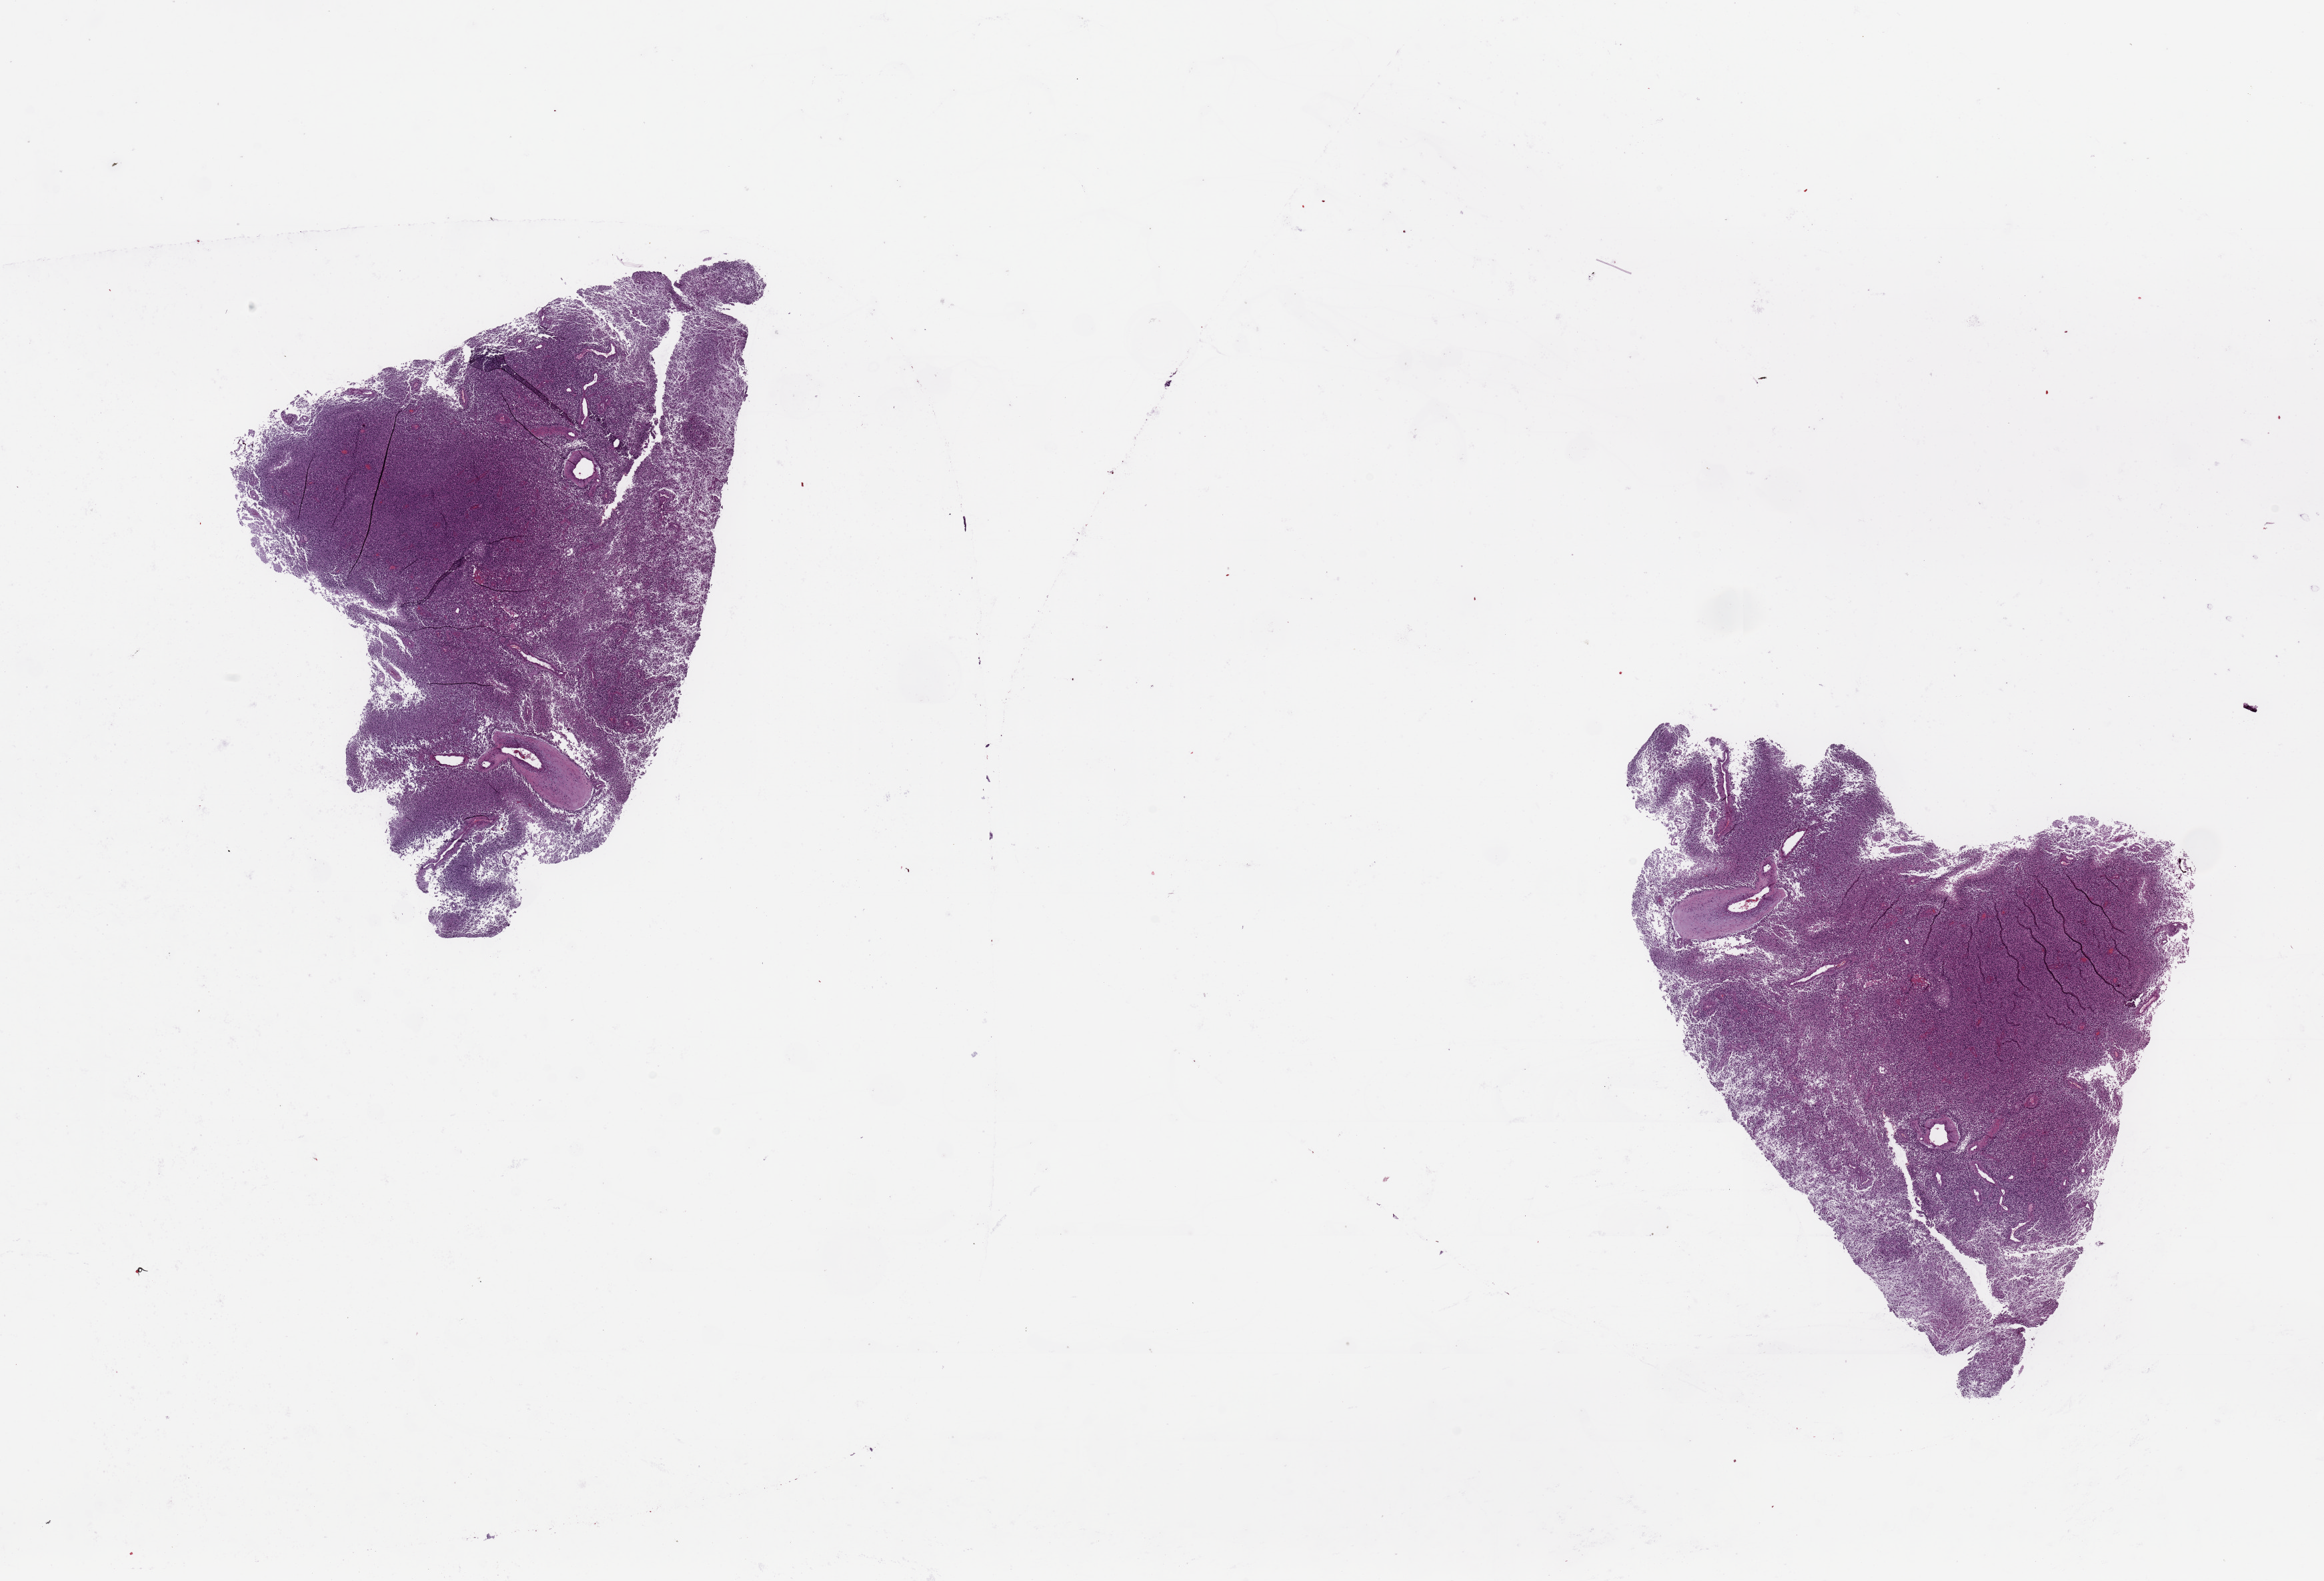
Digitized H&E-stained tissue section (whole slide), shown as a low-resolution overview of the whole scanned area (about 27.6 x 18.8 mm). Tumour tissue sample, sampled site: frontal lobe. 70-year-old male patient. Pathologist review of this section (percent, as recorded): tumour nuclei 70%, necrosis 20%.
Histologic diagnosis: Glioblastoma.